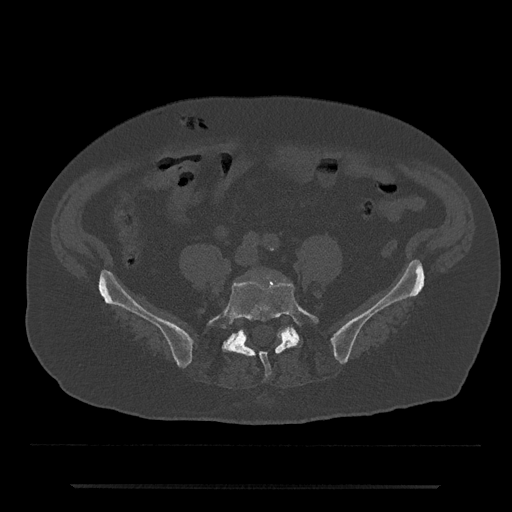
CT including the spine, one axial slice; 120 kVp; bone window (W 1800 / L 400 HU); 512 × 512 image matrix. Patient: male, 80 years. From the clinical record (not read from this slice): primary cancer: prostate.
Annotated regions visible in this slice (semi-automatically segmented with operator editing):
- L5 vertebra: bounding box (x1, y1, x2, y2) in pixels: (207, 281, 319, 377)